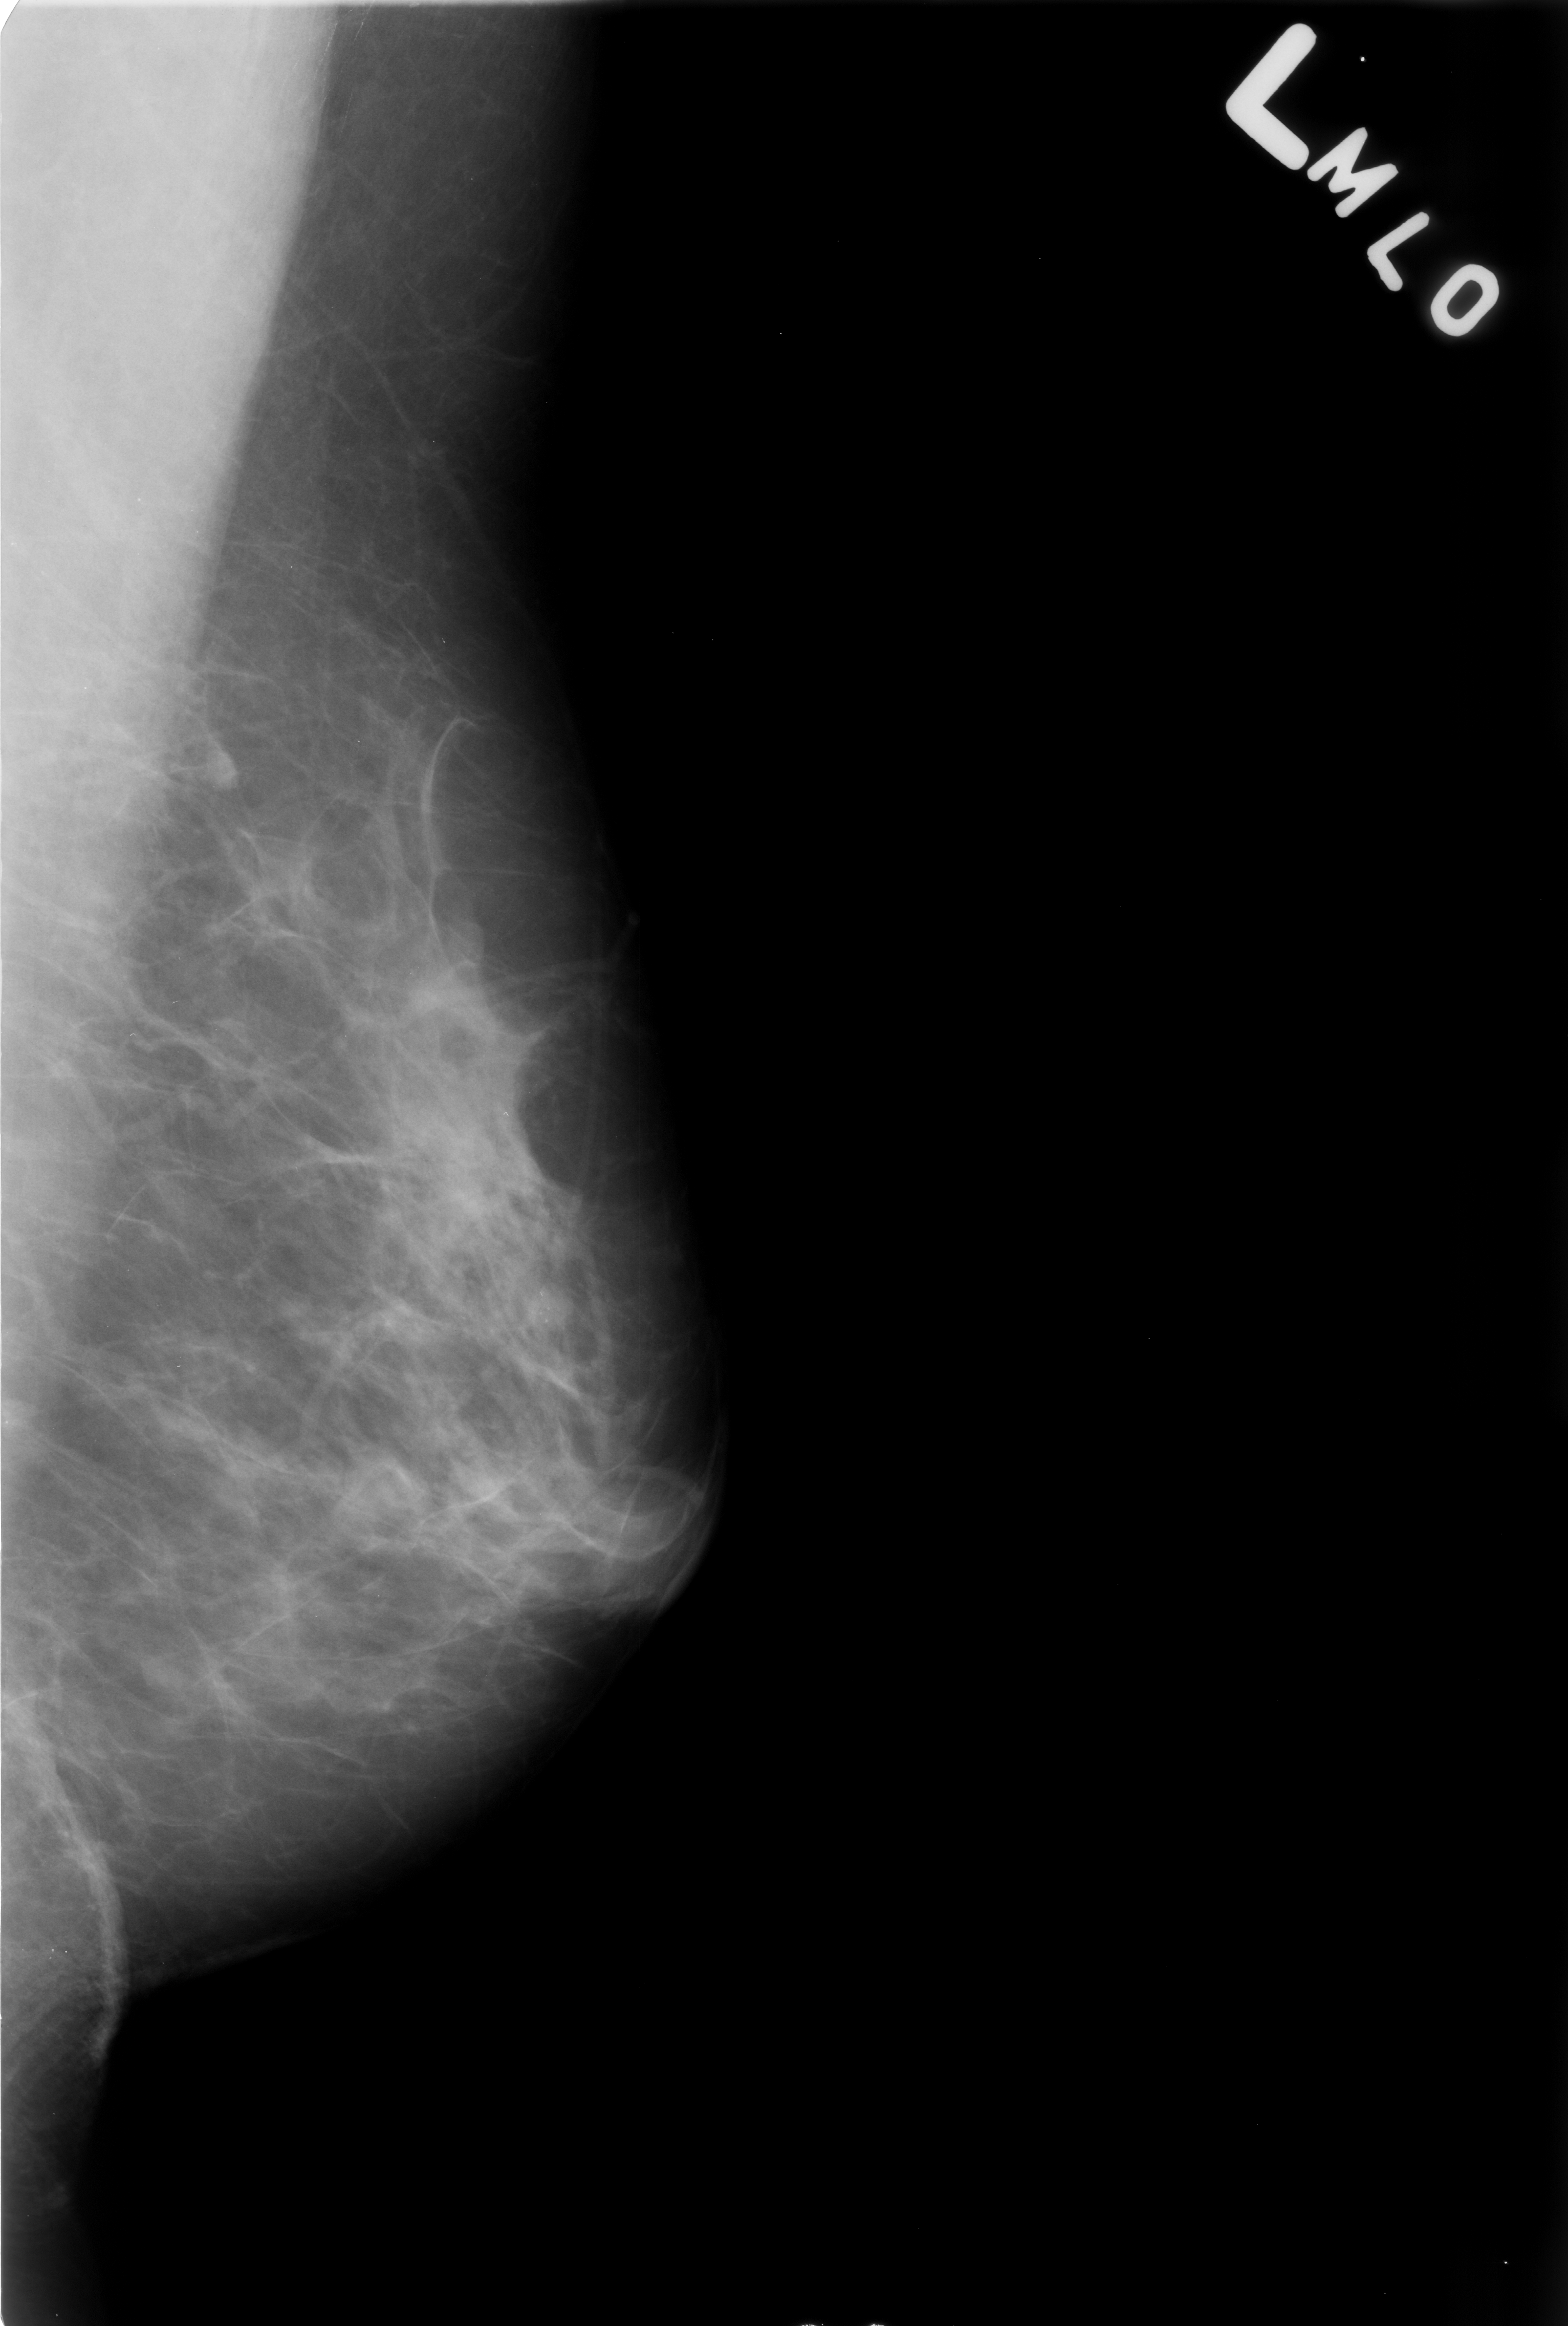
Digitized screen-film mammogram; left breast; mediolateral oblique (MLO) view; breast composition: scattered fibroglandular densities (BI-RADS density category 2 of 4); 1568 × 2326 image matrix.
Expert-marked regions of interest on this image (one box per marked abnormality):
- calcifications, morphology punctate / pleomorphic, distribution clustered; BI-RADS assessment category 4; subtlety rating 3 on a 1 (subtle) to 5 (obvious) scale; pathology result (as recorded, not read from the image): benign: box from (x=507, y=1277) to (x=591, y=1352) px